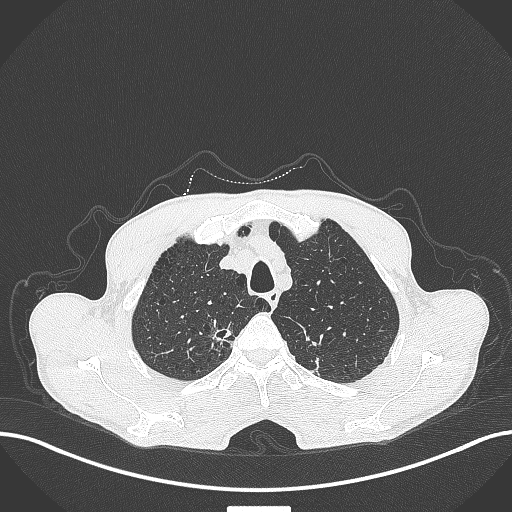
Chest CT, one axial slice. Slice 361 of 445 in the series (ordered by position). Lung window (W 1500 / L -600 HU). 512 × 512 image matrix, field of view 400 × 400 mm. Patient: male, 70 years. From the clinical record (not read from this slice): clinical TNM (as recorded): T1a N0 M0; histopathological grade: G1-2.
Annotated regions visible in this slice (rectangle marked by the reading radiologist):
- lung tumour (recorded histology: adenocarcinoma): bounding box [x1, y1, x2, y2] px = [210, 323, 235, 343]